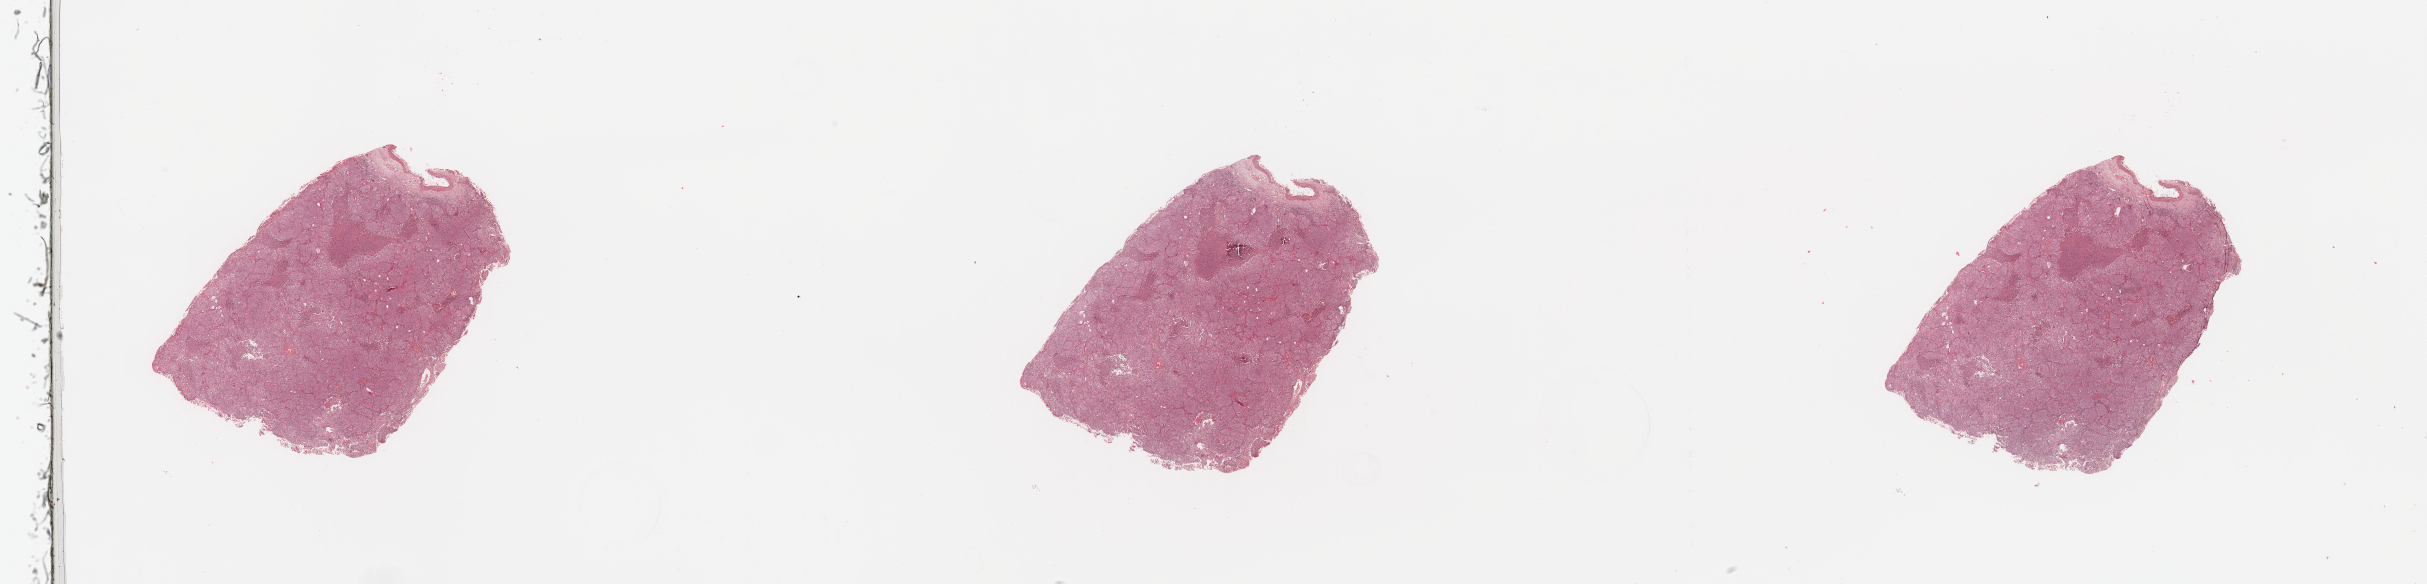
H&E-stained whole-slide image, low-resolution overview of the scanned area, about 38.4 x 9.2 mm (slide scanned at 20x), lung, tumour tissue. Patient: male, age 71 years.
Patient diagnosis (cohort enrolment): squamous cell carcinoma (lung).